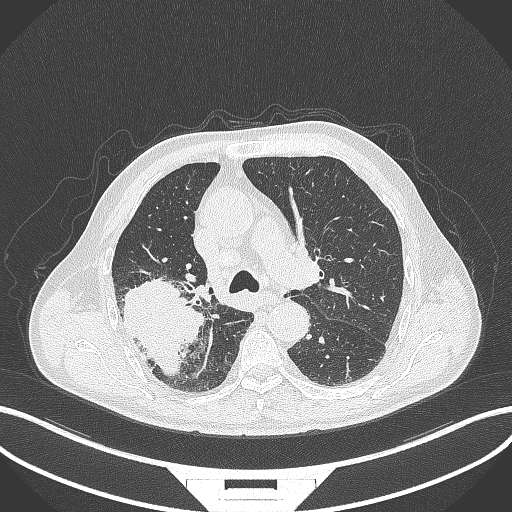
Chest CT, one axial slice; slice 269 of 429 in the series (ordered by position); reconstruction kernel B70f; 120 kVp; lung window (W 1500 / L -600 HU); 1 mm slice thickness; 512 × 512 image matrix. Male patient, age 72 years. Case-level facts recorded for this patient, not image findings: clinical TNM (as recorded): T3 N2 M0.
Structures marked on this image (rectangle marked by the reading radiologist):
- lung tumour (recorded histology: adenocarcinoma): bounding box <119,276,207,385> (left, top, right, bottom; pixels)